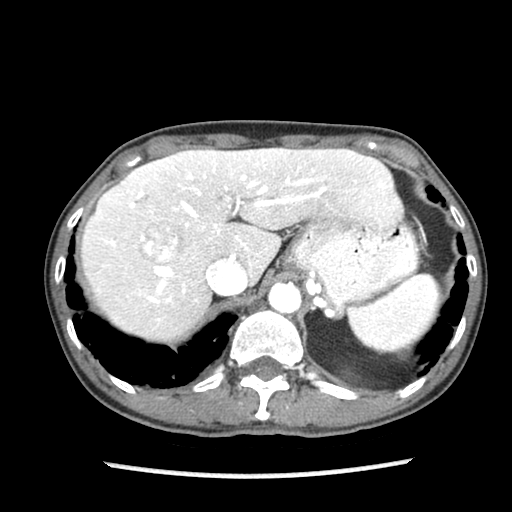
Contrast-enhanced abdominal CT (liver protocol), one axial slice. Position 63 of 87 along the scan axis. Reconstruction kernel STANDARD. 140 kVp. Soft-tissue window (W 400 / L 40 HU). 2.5 mm slice thickness. 512 × 512 image matrix, field of view 300 × 300 mm. From the clinical record (not read from this slice): diagnosis: hepatocellular carcinoma (patient treated with transarterial chemoembolisation; whether this scan precedes or follows treatment is not stated here); TNM stage (as recorded): Stage-IIIB; Child-Pugh class: A.
Outlined on this slice (semi-automatic segmentation, software-assisted and operator-edited):
- liver parenchyma outside the tumour (the mass and vessels are separate outlines, so this box may not span the whole liver): bounding box (x1, y1, x2, y2) in pixels: (82, 148, 402, 340)
- mass: (145, 230, 182, 262)
- liver vessels: (110, 175, 384, 303)